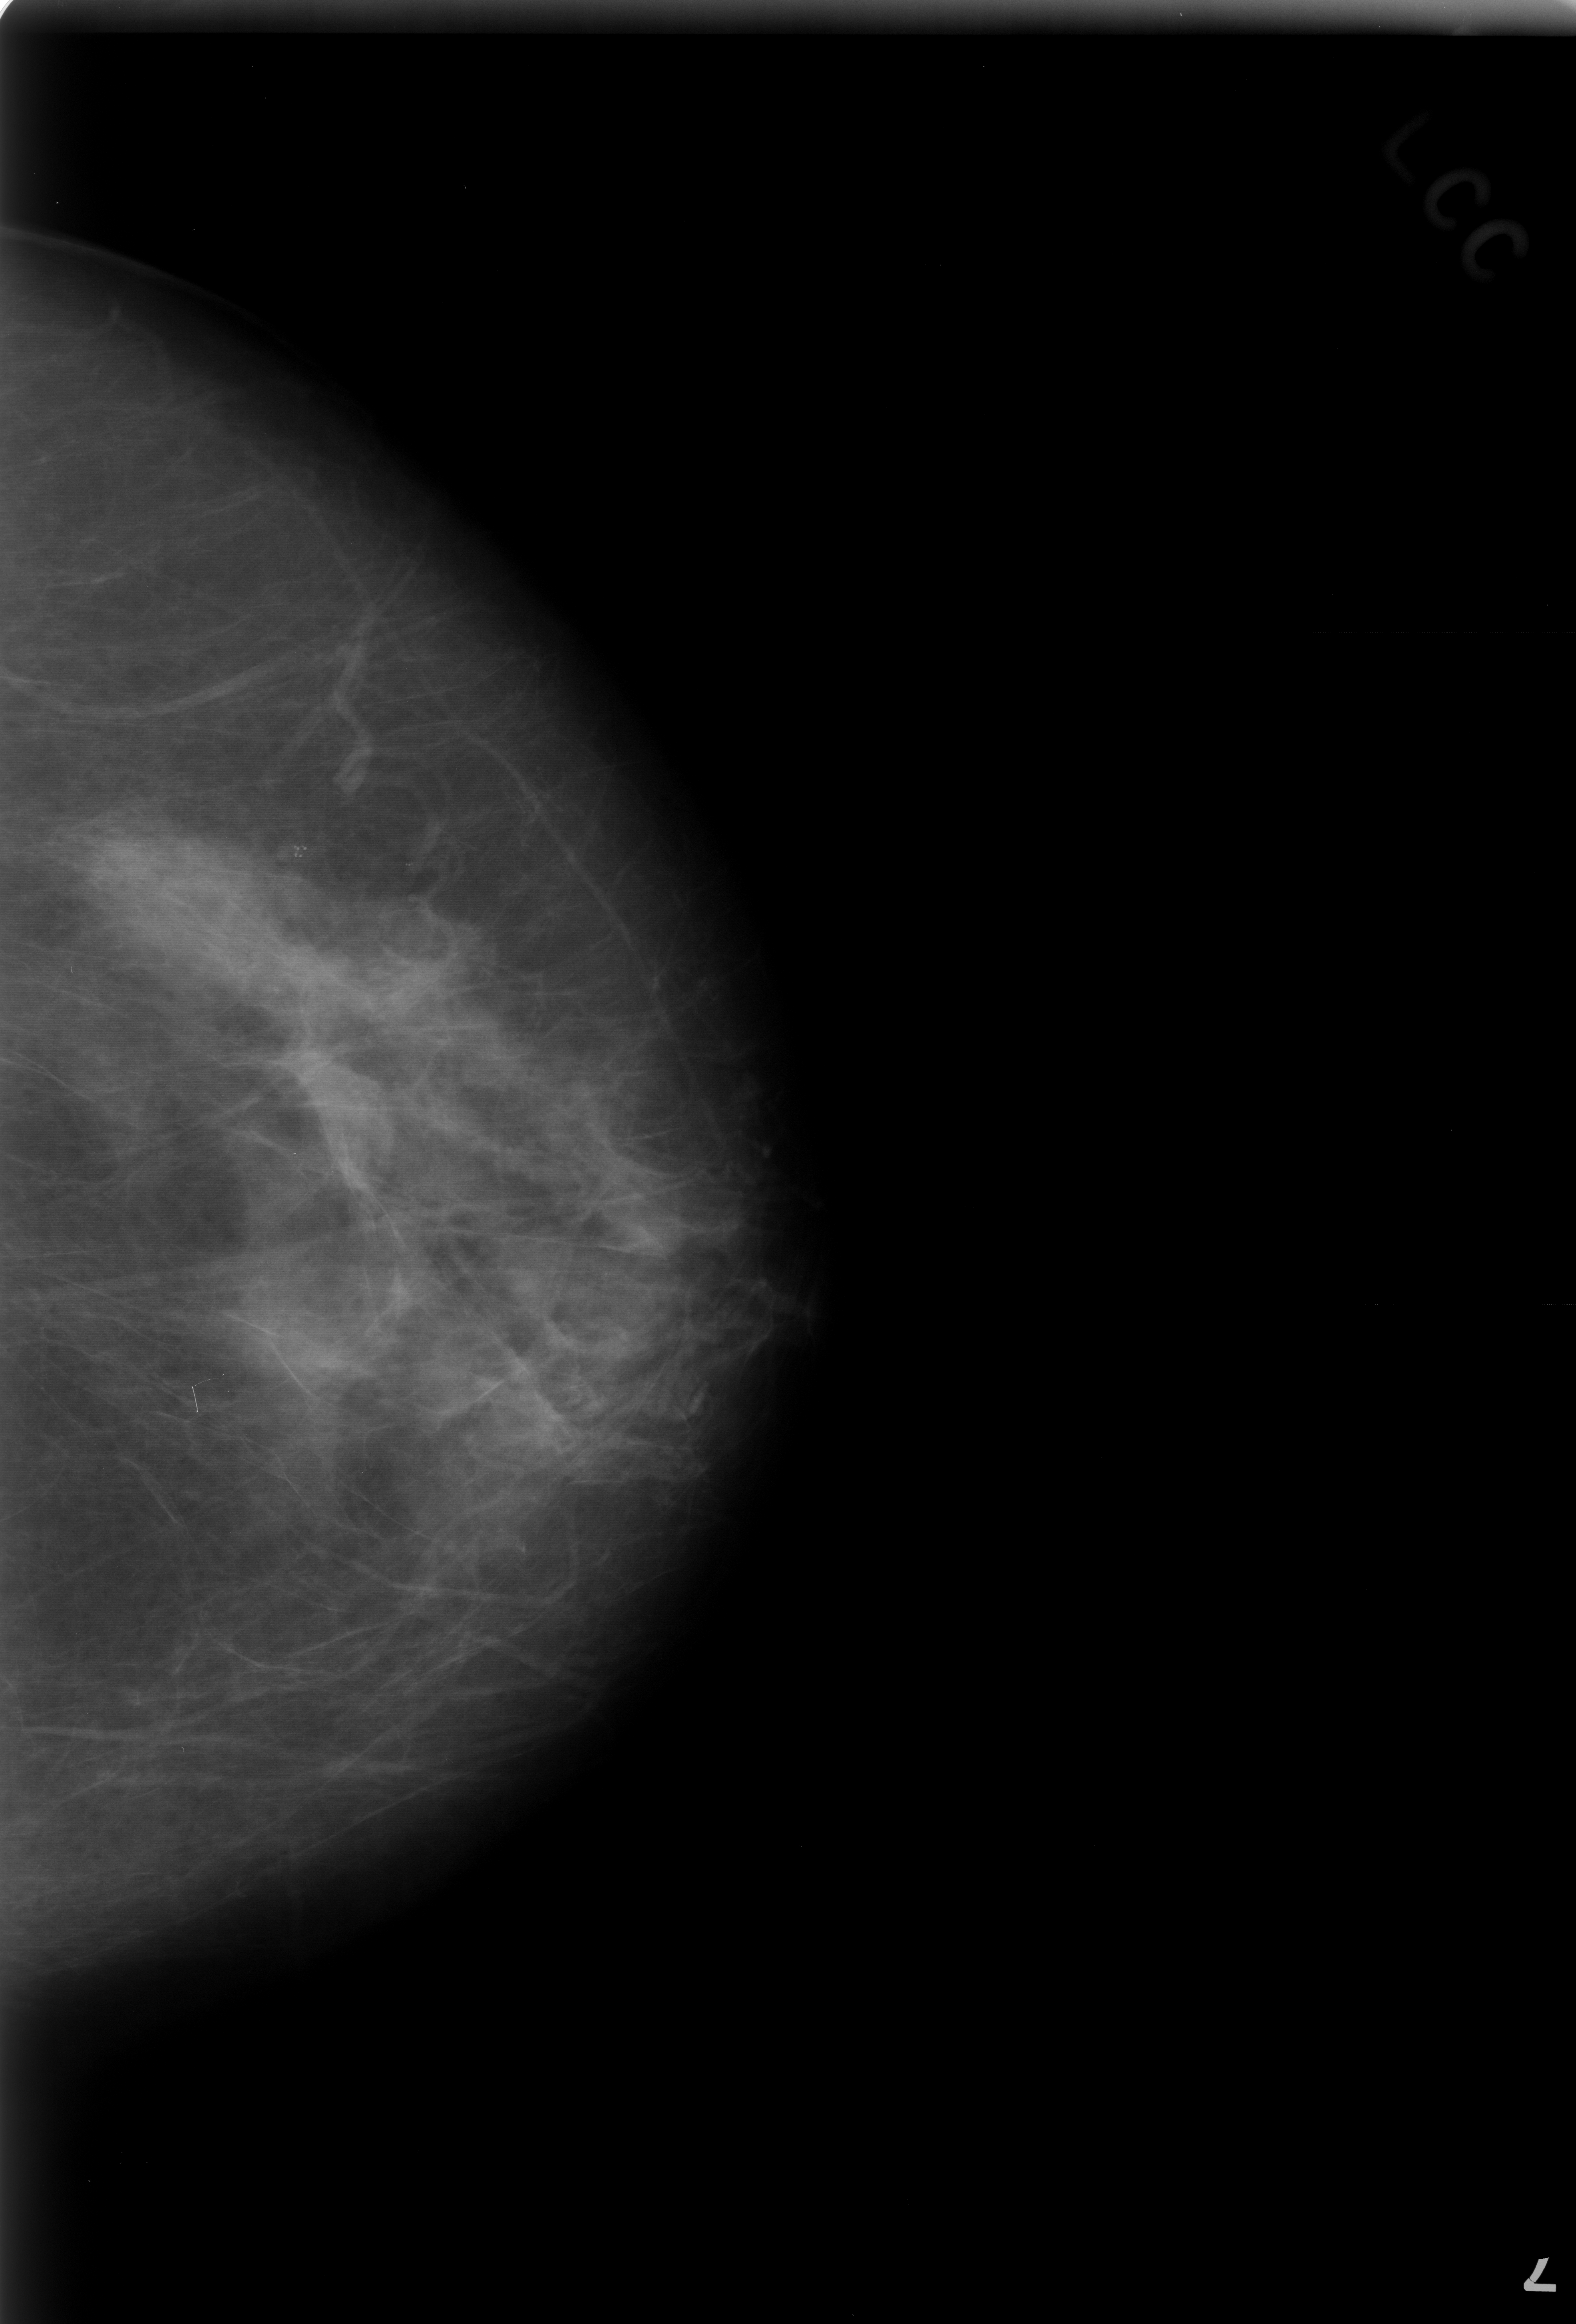
Mammogram (digitized film), left breast, craniocaudal (CC) view, breast composition: scattered fibroglandular densities (BI-RADS density category 2 of 4).
Radiologist-marked abnormalities on this image: calcifications, morphology punctate, distribution clustered; BI-RADS assessment category 3; subtlety rating 4 on a 1 (subtle) to 5 (obvious) scale; pathology (as recorded): benign.